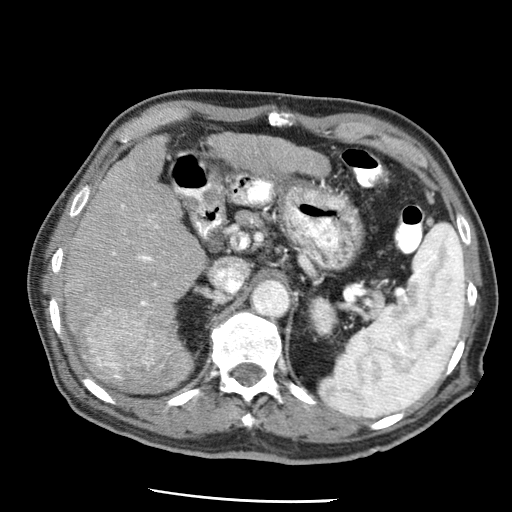
Contrast-enhanced abdominal CT (liver protocol), one axial slice. Position 30 of 79 along the scan axis. Reconstruction kernel STANDARD. 120 kVp. Soft-tissue window (W 400 / L 40 HU). 512 × 512 image matrix, field of view 320 × 320 mm. Case-level facts recorded for this patient, not image findings: diagnosis: hepatocellular carcinoma (patient treated with transarterial chemoembolisation; whether this scan precedes or follows treatment is not stated here); TNM stage (as recorded): Stage-IIIA; Child-Pugh class: A.
Outlined on this slice (semi-automatically segmented with operator editing):
- liver parenchyma outside the tumour (the mass and vessels are separate outlines, so this box may not span the whole liver): box from (x=60, y=136) to (x=206, y=392) px
- mass: (x=65, y=266)–(x=155, y=372)
- liver vessels: (x=112, y=204)–(x=169, y=379)